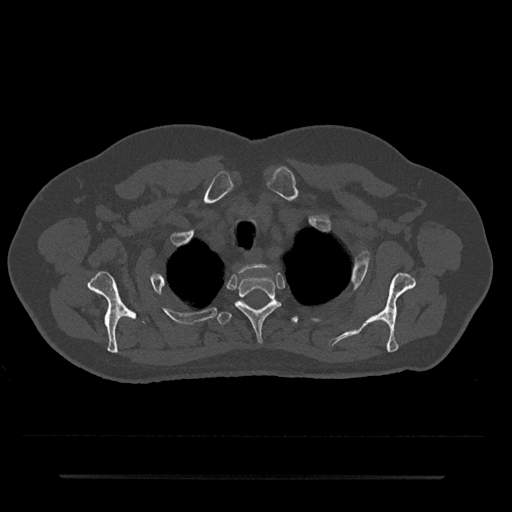
CT including the spine, one axial slice; position 600 of 797 along the scan axis; 120 kVp; bone window (W 1800 / L 400 HU); 0.5 mm slice thickness; 512 × 512 image matrix, field of view 437 × 437 mm. Male patient, age 69 years. From the clinical record (not read from this slice): primary cancer: prostate.
Outlined on this slice (semi-automatic segmentation, software-assisted and operator-edited):
- T1 vertebra: bounding box <239,264,264,275> (left, top, right, bottom; pixels)
- T2 vertebra: <235,275,281,342>
- T3 vertebra: <217,301,298,325>